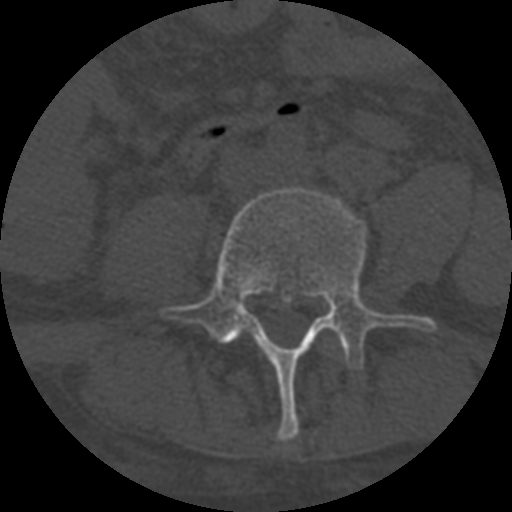
CT including the spine, one axial slice; slice 211 of 708 in the series (ordered by position); one of 3 acquisitions stored at this slice position; bone window (W 1800 / L 400 HU); 1.25 mm slice thickness; 512 × 512 image matrix, field of view 160 × 160 mm. Patient age 55 years. From the clinical record (not read from this slice): primary cancer: colon.
Structures marked on this image (semi-automatic segmentation, software-assisted and operator-edited):
- L4 vertebra: bounding box [x1, y1, x2, y2] px = [162, 187, 437, 442]